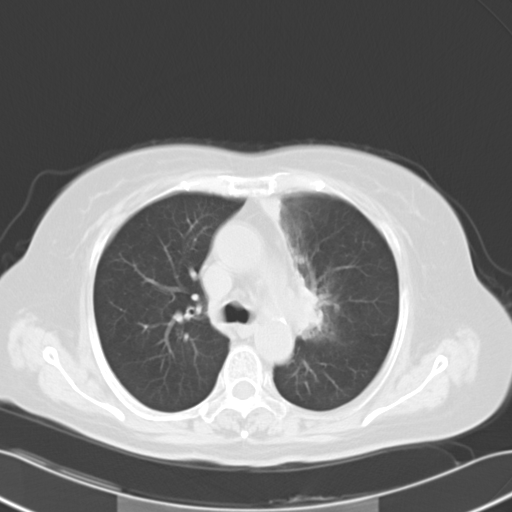
Chest CT, one axial slice; slice 19 of 28 in the series (ordered by position); reconstruction kernel B40f; lung window (W 1500 / L -600 HU); 10 mm slice thickness; 512 × 512 image matrix, field of view 353 × 353 mm. Patient: female, 65 years. From the clinical record (not read from this slice): clinical TNM (as recorded): T2b N1 M0.
Annotated regions visible in this slice (bounding box drawn by a radiologist):
- lung tumour (recorded histology: adenocarcinoma): bounding box (x1, y1, x2, y2) in pixels: (300, 277, 326, 341)